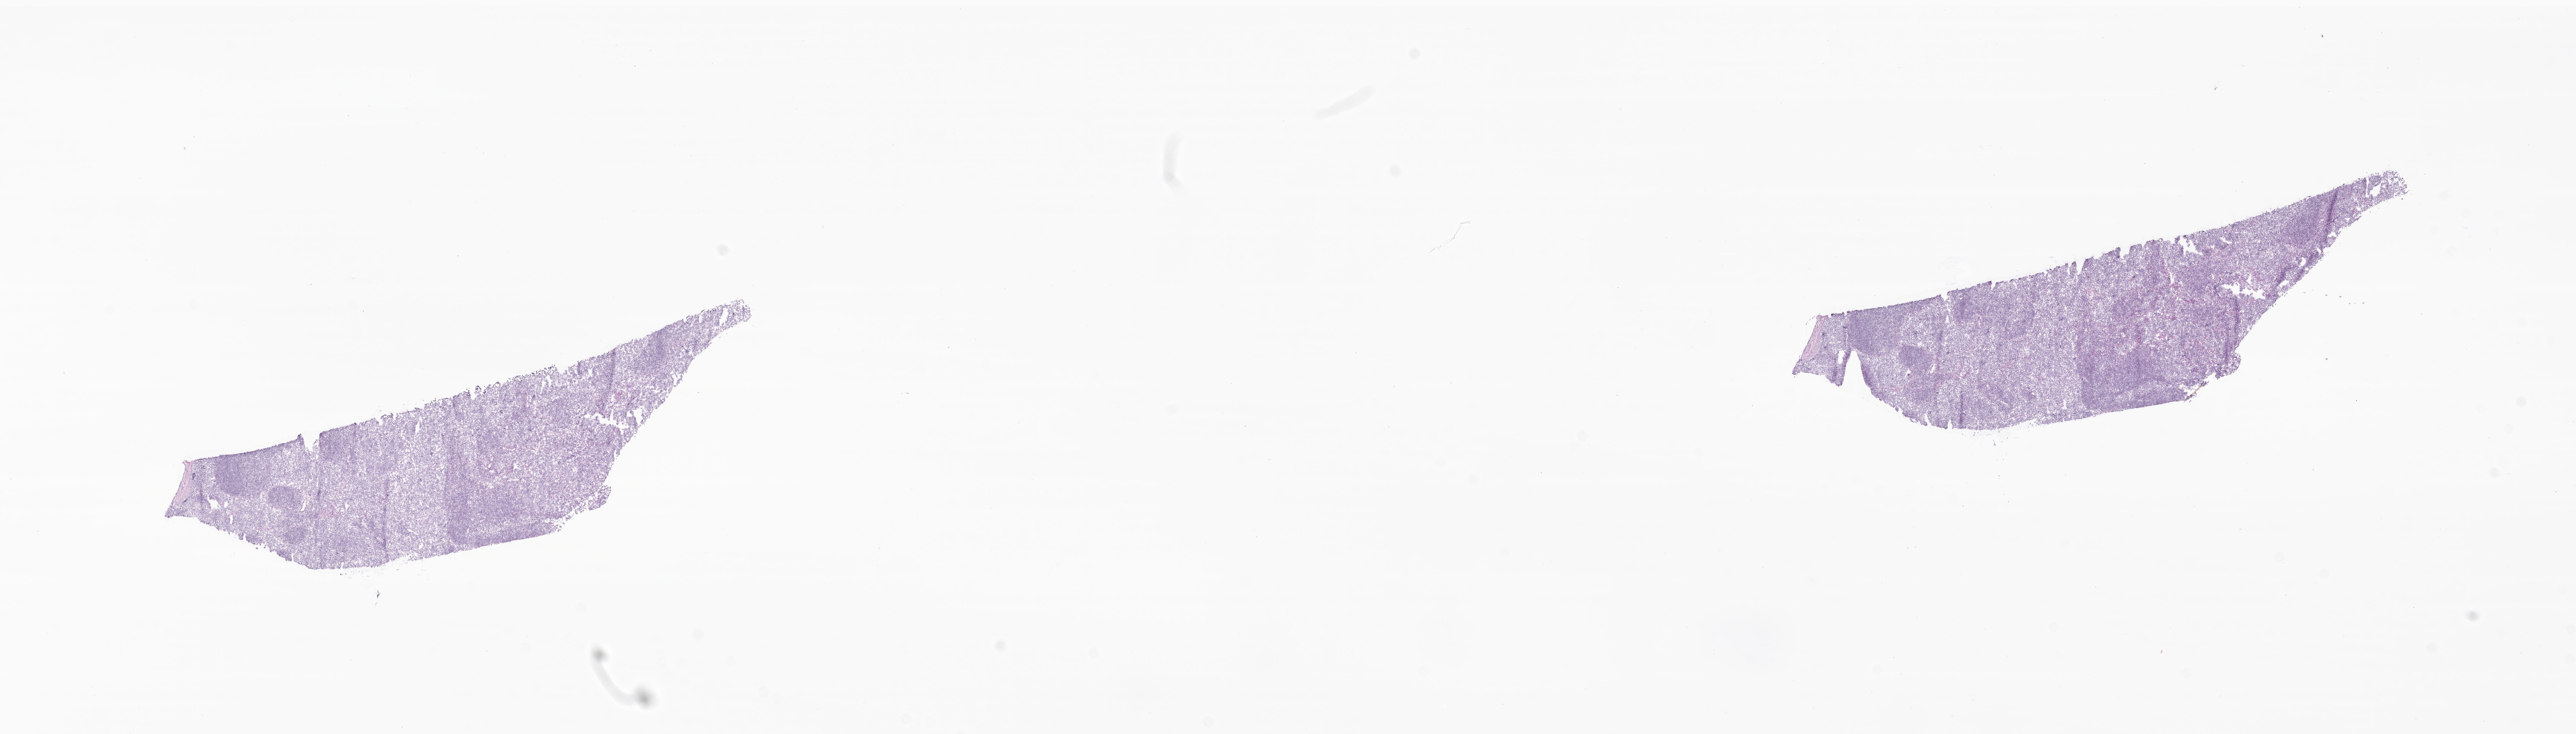
Hematoxylin and eosin (H&E) whole-slide image of tumor tissue from the head and neck — shown as a low-resolution overview of the whole scanned area (about 28.4 x 8.1 mm); cryosection (OCT / tissue freezing medium). Male patient, age 340 days.
• recorded diagnosis: Neuroblastoma, NOS
• tissue or organ of origin (case record): head, face or neck